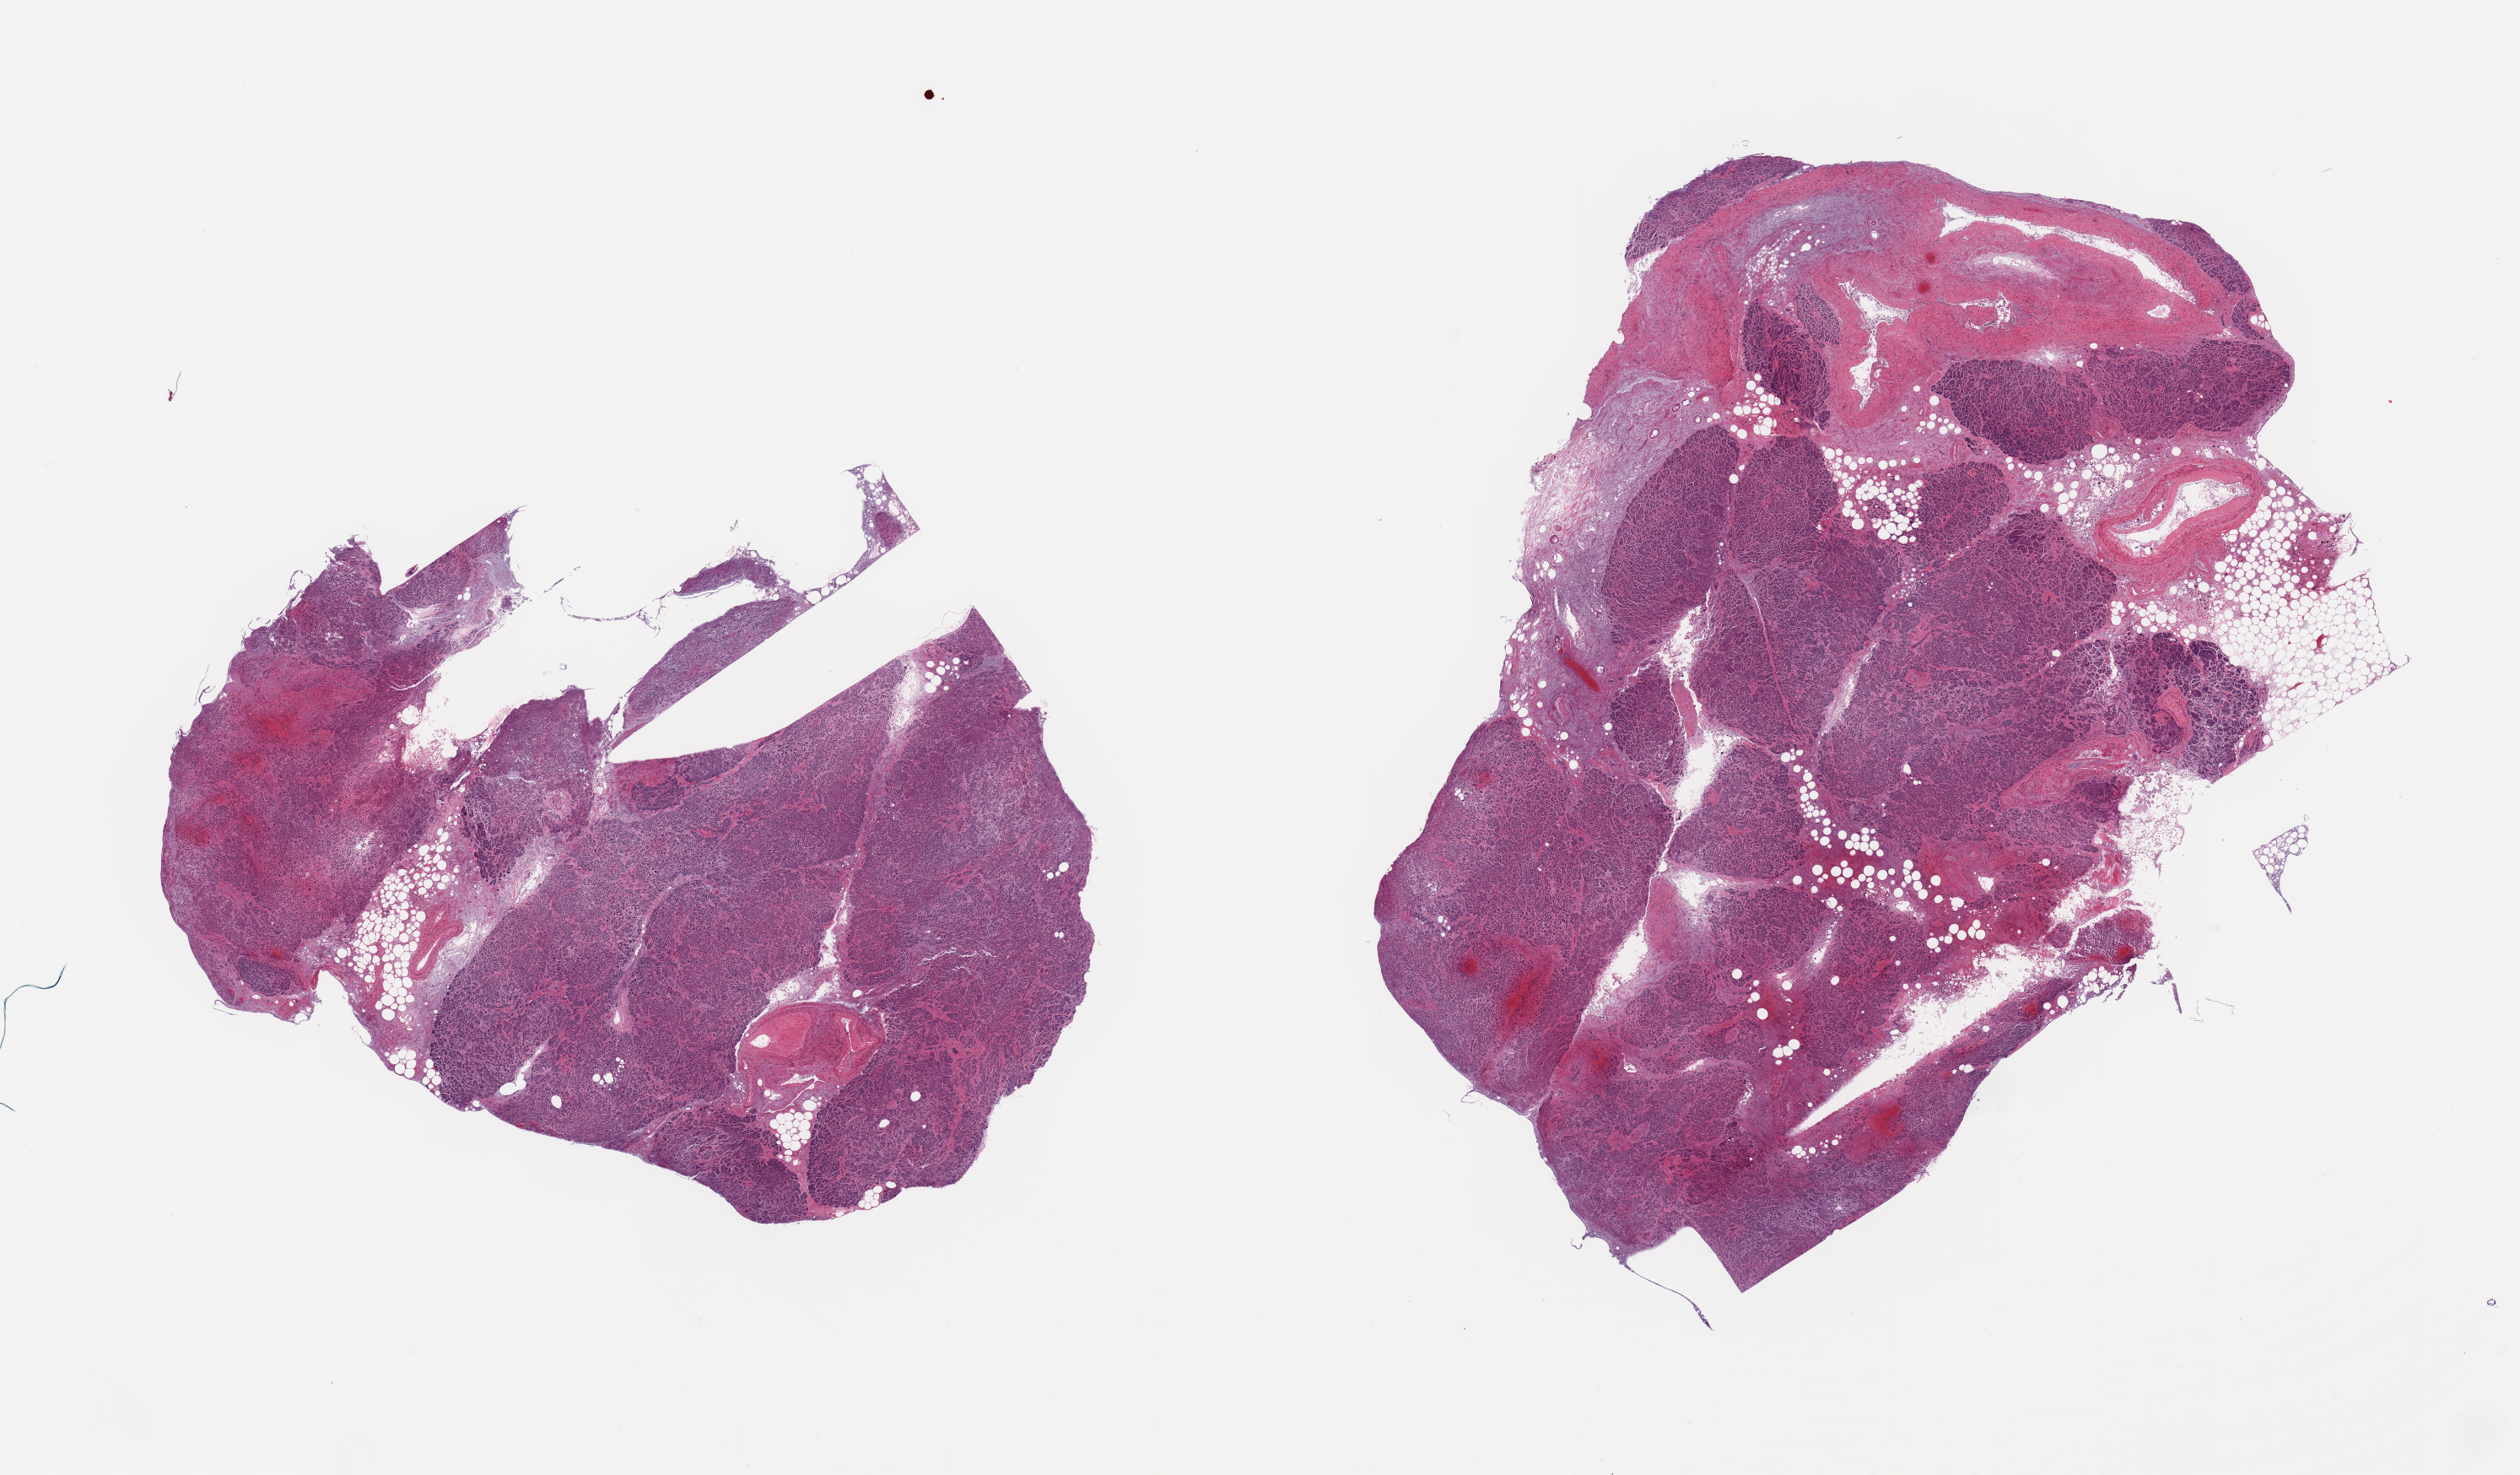
Hematoxylin and eosin (H&E) whole-slide image, shown as a low-resolution overview of the whole scanned area (about 23.6 x 13.8 mm); PAXgene-fixed paraffin-embedded (PFPE) section; target tissue: pancreas; donor tissue sample. Male donor.
- reviewer comment on this tissue sample: 2 pieces; small focal areas moderately autolyzed, but most is severely autolyzed